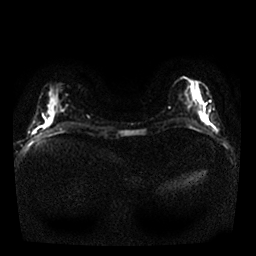
Breast MRI, one axial slice. Position 11 of 25 along the scan axis. Diffusion-weighted series; image 2 of 4 stored at this slice position (different b-values; order by instance number). 1.5 T. 256 × 256 image matrix, field of view 320 × 320 mm. Female patient.
Outlined on this slice (expert manual segmentation):
- tumour on diffusion-weighted imaging: box from (x=201, y=115) to (x=208, y=123) px